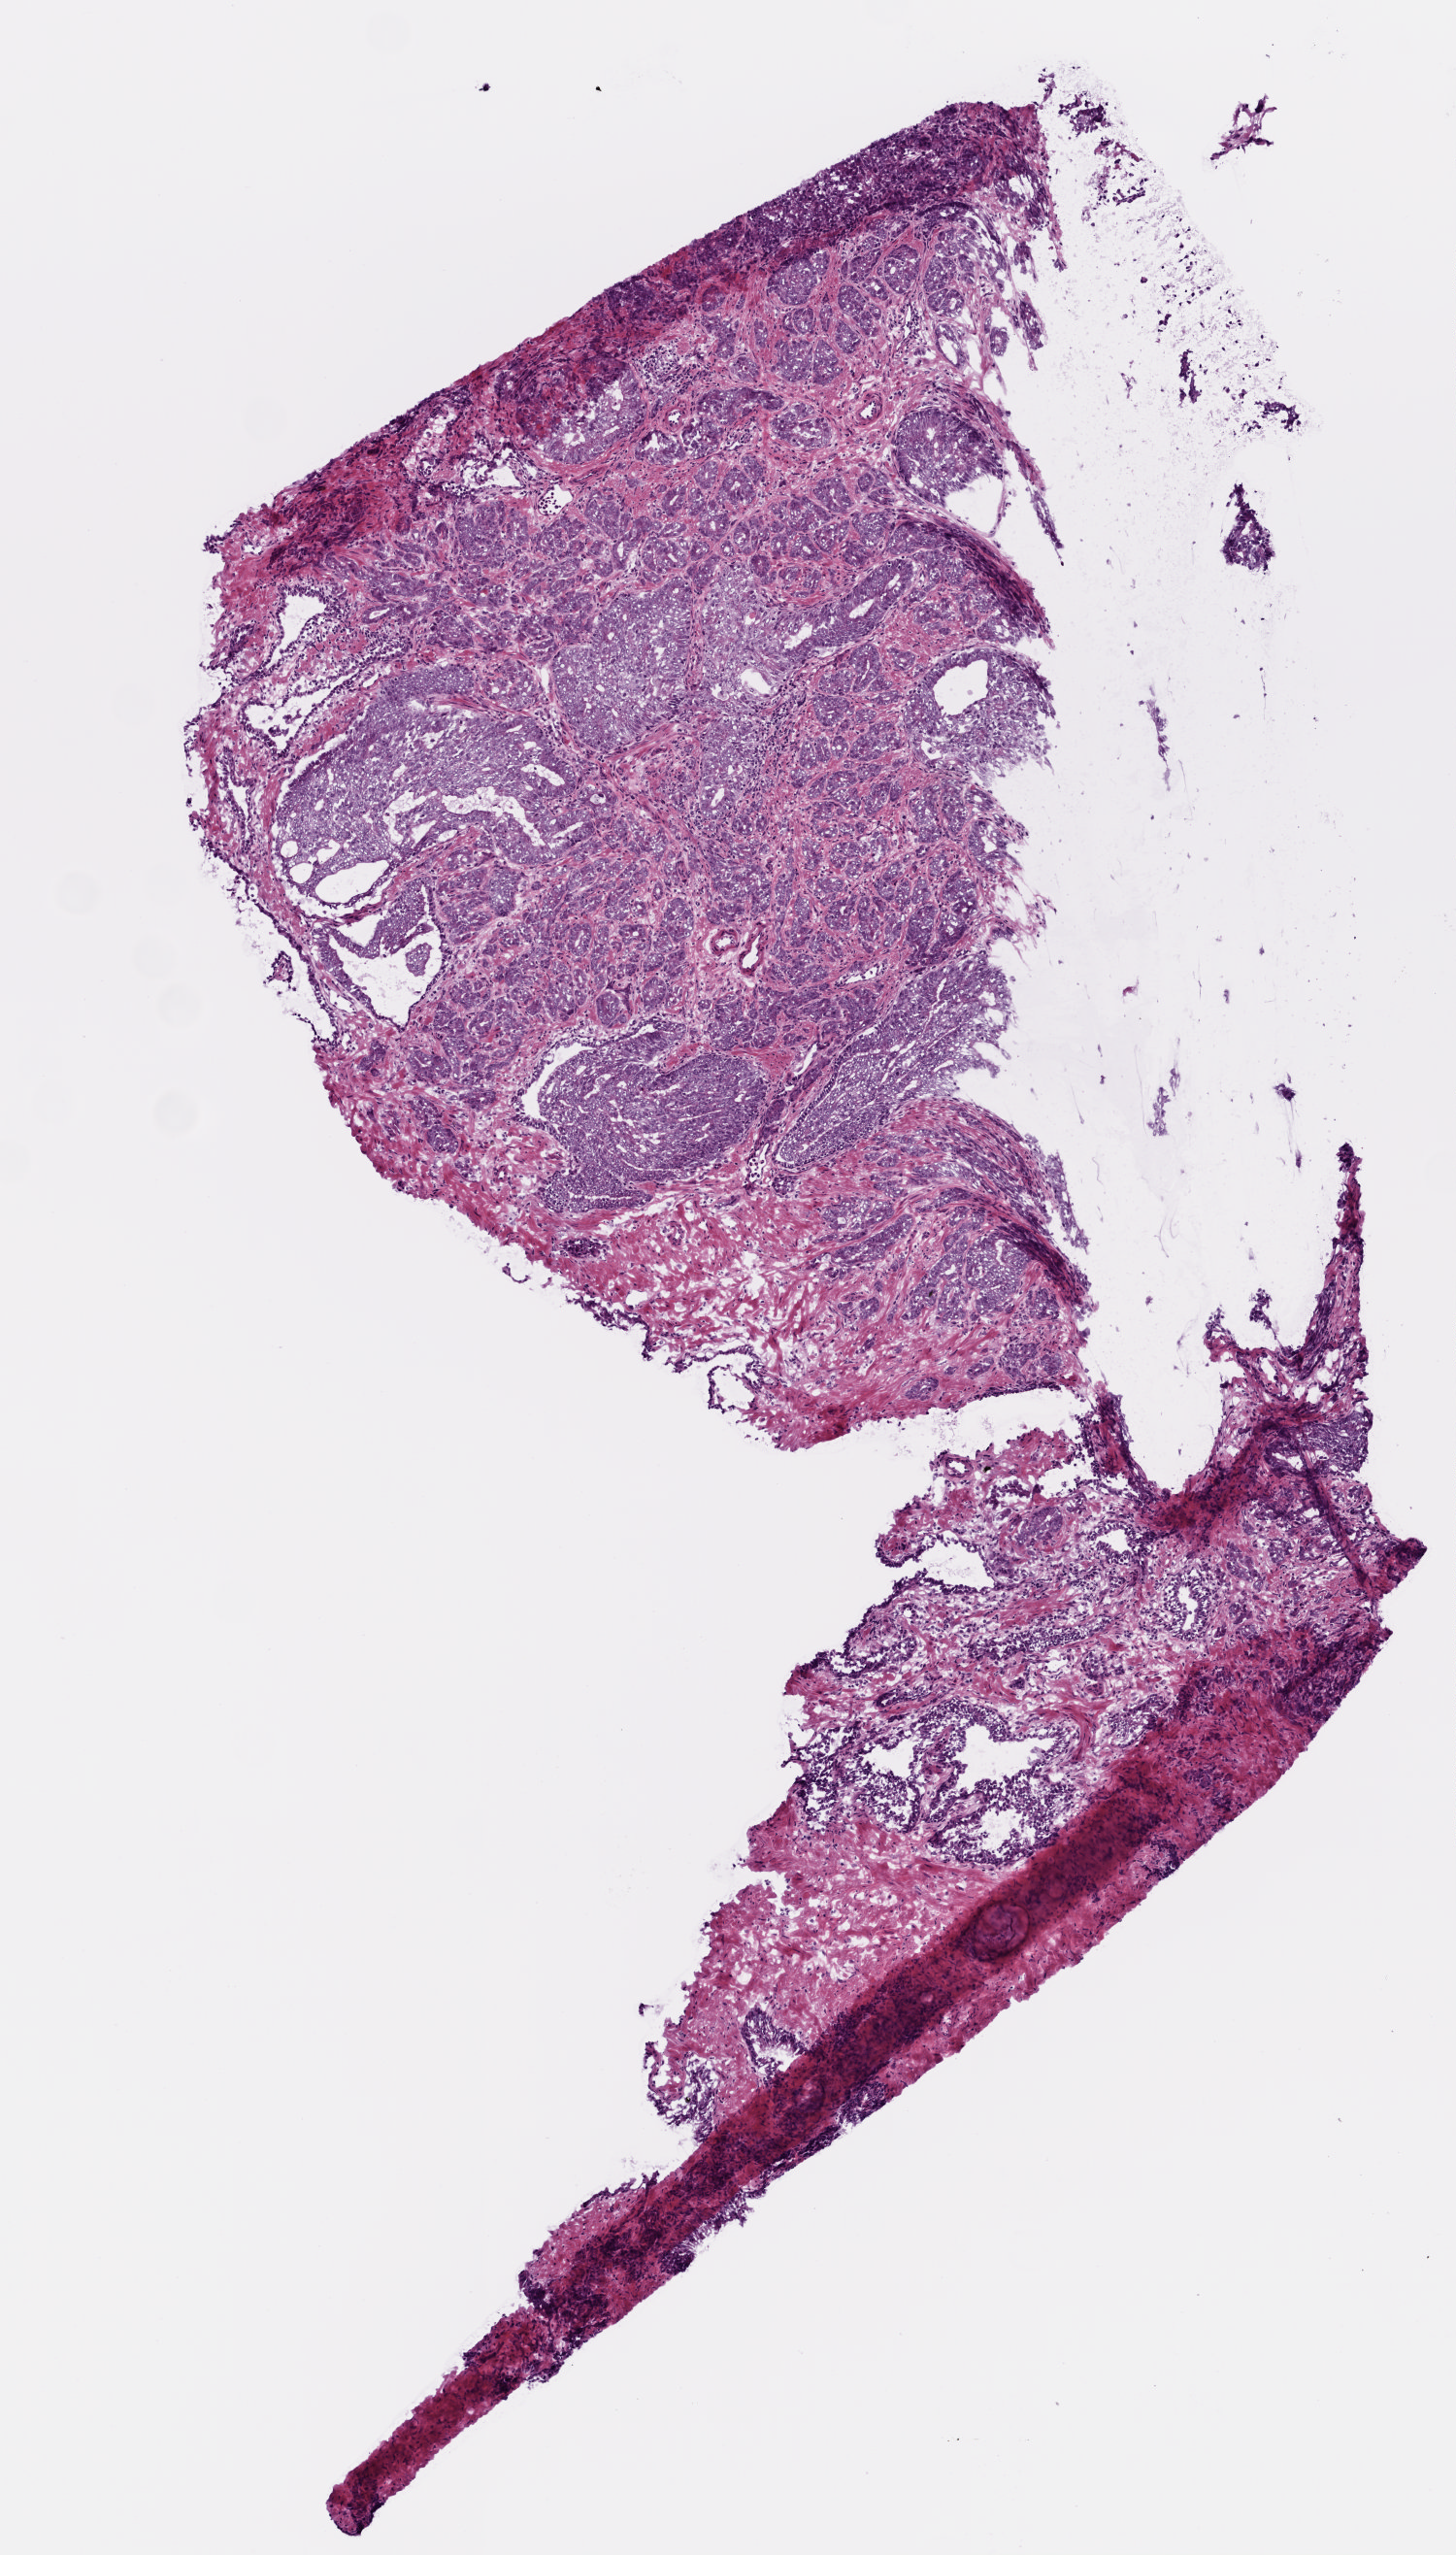
Whole-slide histology image, H&E — low-resolution overview of the scanned area, about 3.0 x 5.3 mm (slide scanned at 20x); frozen section from the bottom of the tissue portion; primary tumour sample from the prostate. Patient: male, age at initial diagnosis 65 years. Gleason score: 7 (3+4). Pathologist review of this section (percent, as recorded): tumour cells 75%, tumour nuclei 75%, normal cells 10%, stromal cells 15%, necrosis 0%. Inflammatory infiltration, as recorded: lymphocyte infiltration 0%, monocyte infiltration 0%, neutrophil infiltration 0%.
Diagnosis: Acinar cell carcinoma (prostate gland). Lymph nodes positive (case pathology): 0 of 4 examined. Laterality: bilateral.